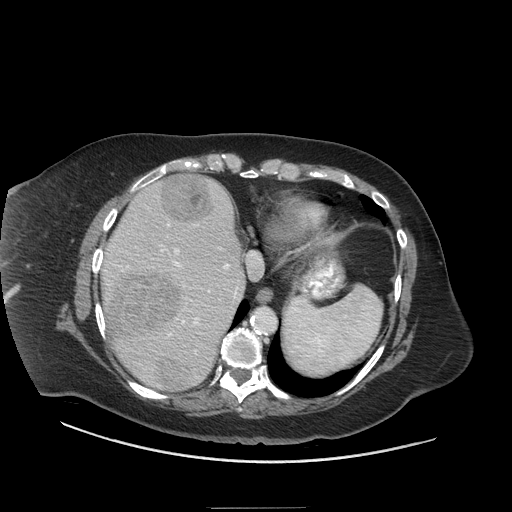
Contrast-enhanced abdominal CT (liver protocol), one axial slice; position 54 of 81 along the scan axis; reconstruction kernel STANDARD; soft-tissue window (W 400 / L 40 HU); 2.5 mm slice thickness; 512 × 512 image matrix, field of view 440 × 440 mm. Case-level facts recorded for this patient, not image findings: diagnosis: hepatocellular carcinoma (patient treated with transarterial chemoembolisation; whether this scan precedes or follows treatment is not stated here); TNM stage (as recorded): Stage-II; Child-Pugh class: A; tumour differentiation: moderately differentiated; tumour size: 1.7 cm.
Structures marked on this image (semi-automatically segmented with operator editing):
- liver parenchyma outside the tumour (the mass and vessels are separate outlines, so this box may not span the whole liver): bounding box <102,176,244,392> (left, top, right, bottom; pixels)
- mass: <112,172,213,391>
- liver vessels: <105,196,239,386>